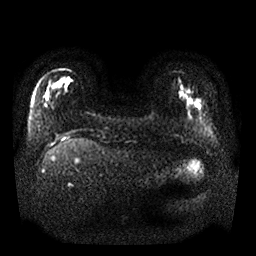
Breast MRI, one axial slice; position 5 of 25 along the scan axis; diffusion-weighted series; image 2 of 4 stored at this slice position (different b-values; order by instance number); 1.5 T; 4 mm slice thickness; 256 × 256 image matrix, field of view 340 × 340 mm. Female patient.
Structures marked on this image (manually delineated by an expert):
- tumour on diffusion-weighted imaging: bounding box [x1, y1, x2, y2] px = [187, 97, 202, 109]